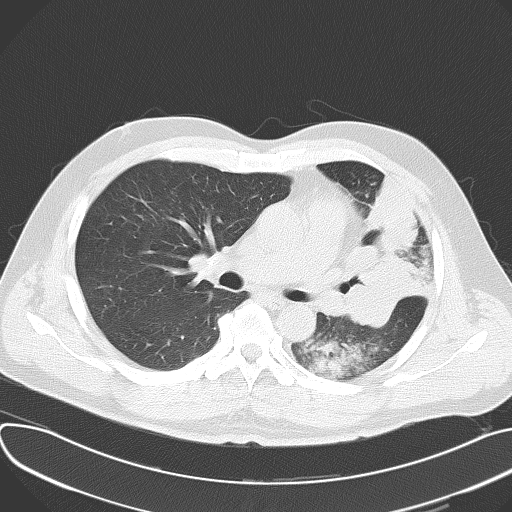
Chest CT, one axial slice. Reconstruction kernel B70f. 120 kVp. Lung window (W 1500 / L -600 HU). 512 × 512 image matrix, field of view 377 × 377 mm. Patient: male, 48 years. From the clinical record (not read from this slice): clinical TNM (as recorded): T4 N0 M0.
Outlined on this slice (rectangle marked by the reading radiologist):
- lung tumour (recorded histology: adenocarcinoma): bounding box <339,172,431,334> (left, top, right, bottom; pixels)